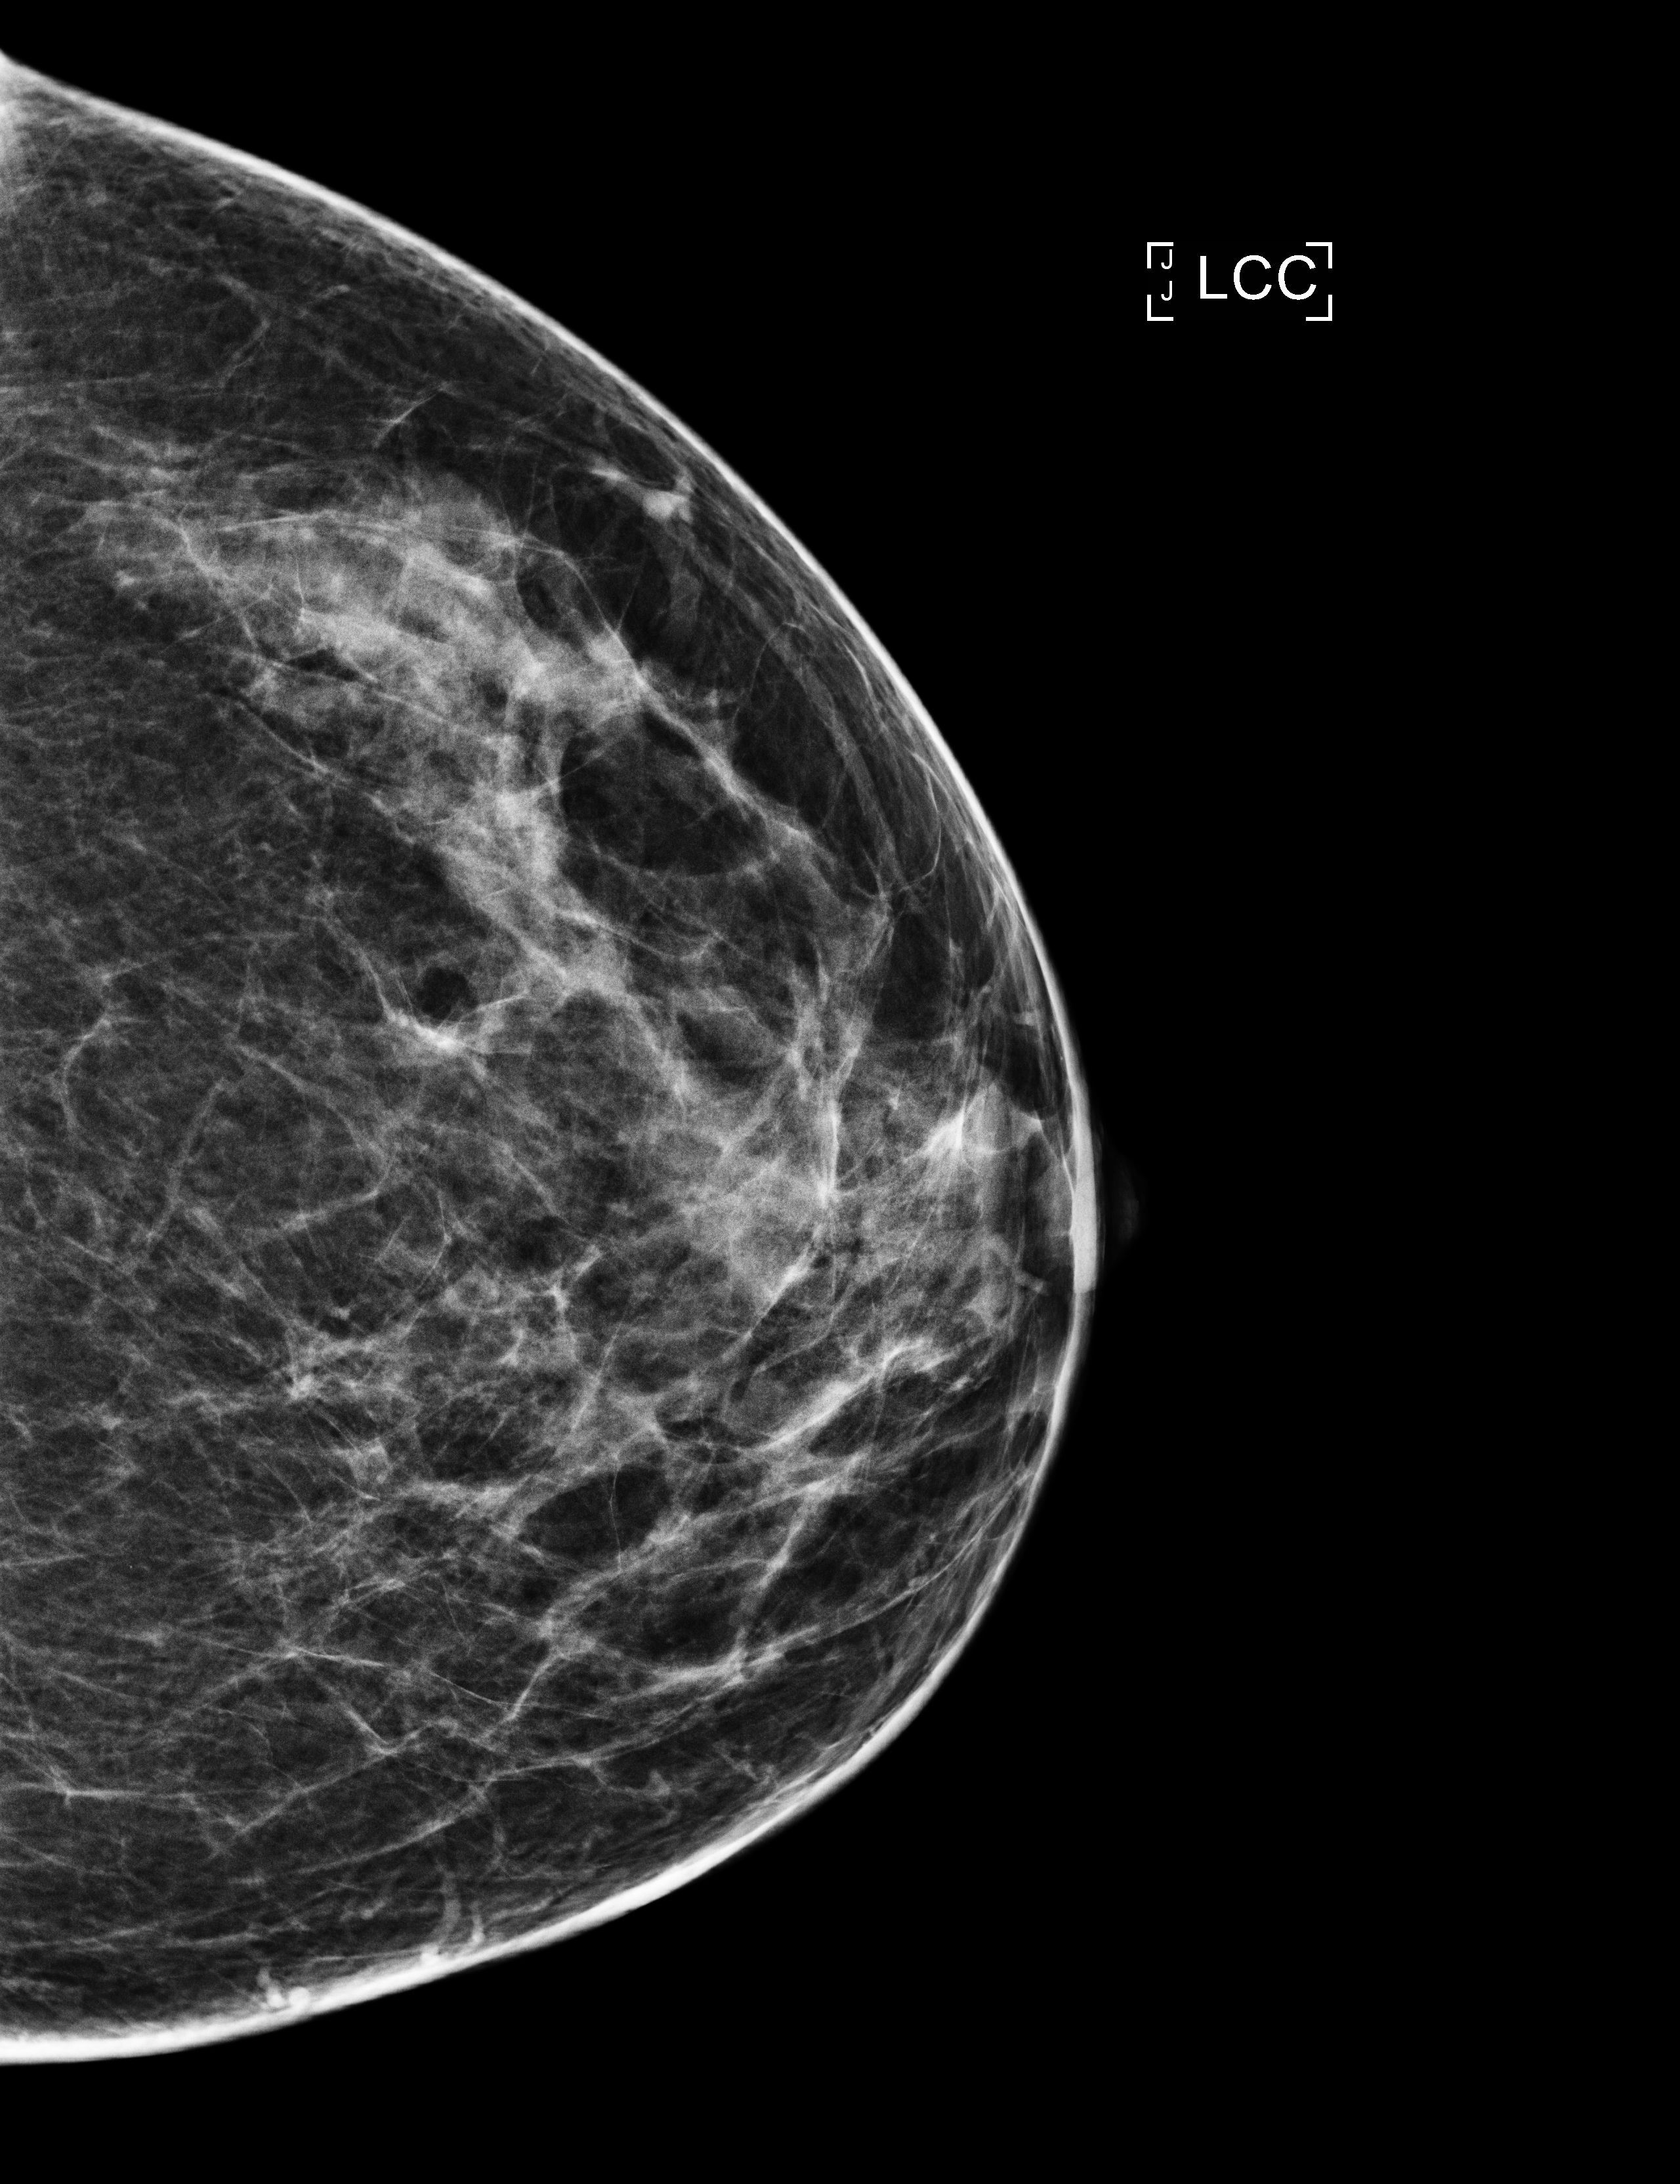
Full-field digital mammogram (FFDM), left breast, CC view, annual screening mammography examination, compressed breast thickness 63 mm, system: Selenia Dimensions. Female patient, age 53 years.
Breast density at the screening exam (both breasts): scattered fibroglandular densities (BI-RADS density category b). Final BI-RADS category for the screening round (tomosynthesis exam, both breasts): category 1. Recall: no recall after this screen.